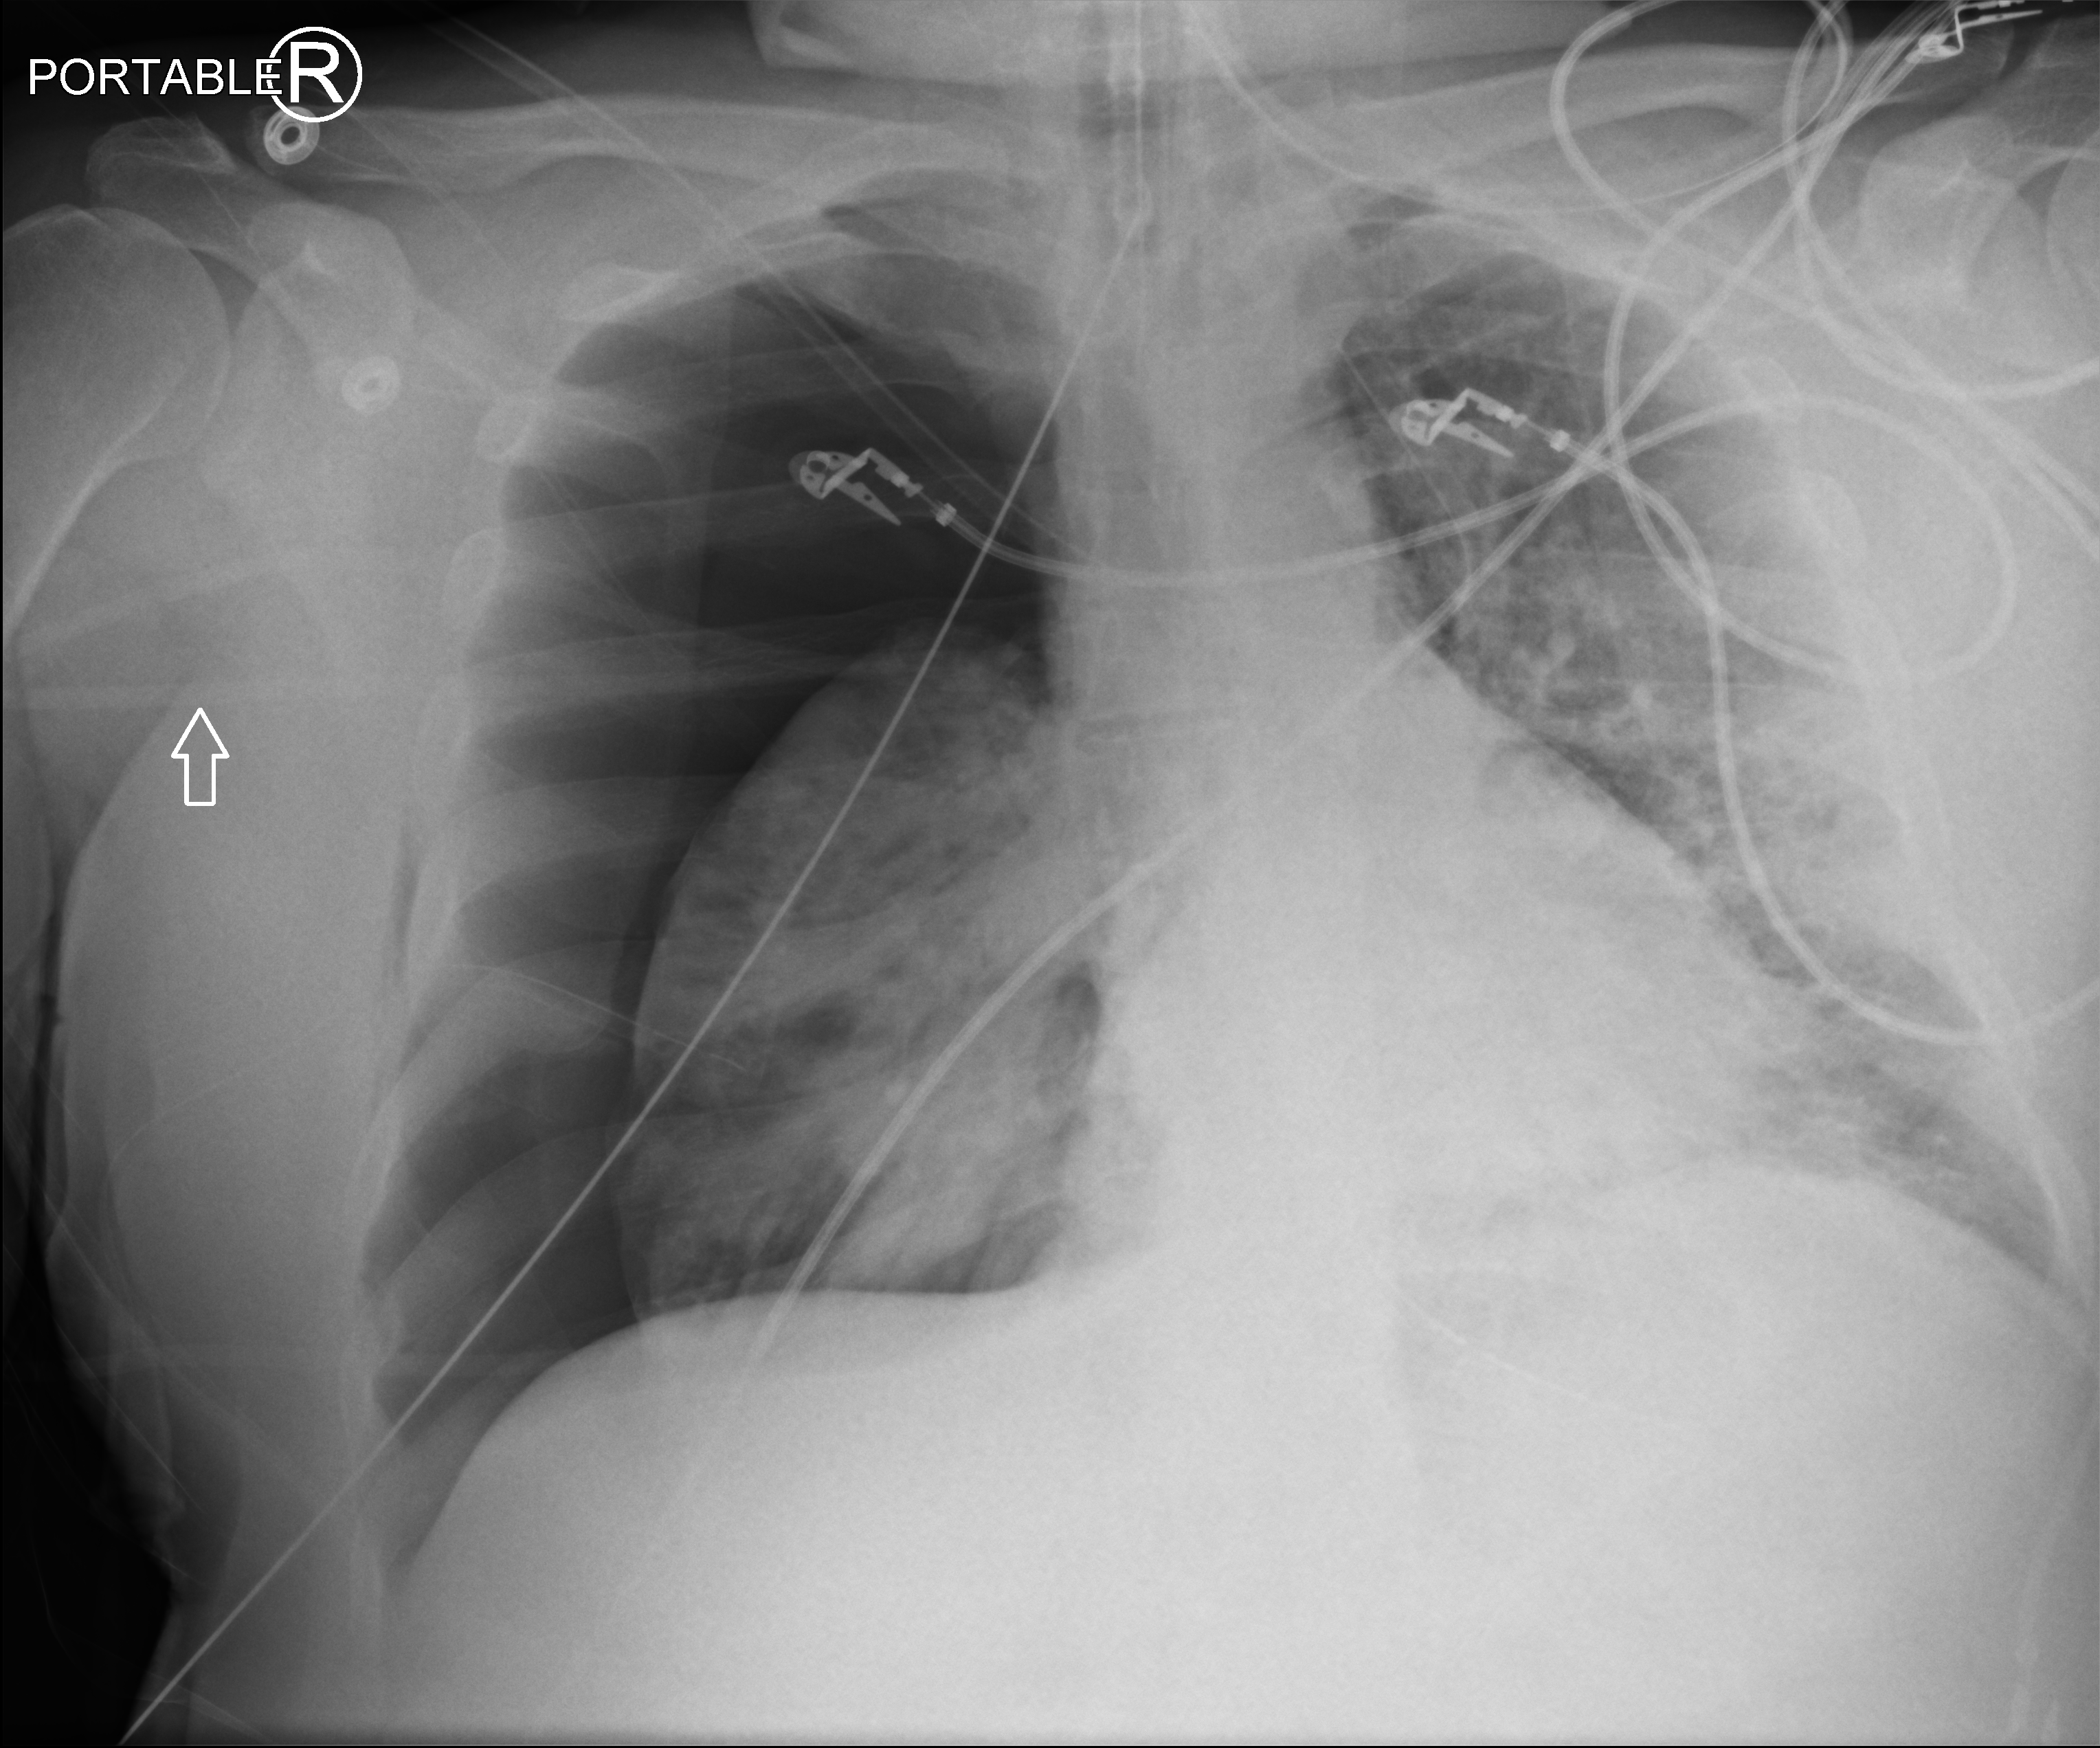
Portable chest radiograph; anteroposterior (AP) projection. Patient hospitalised with COVID-19; male, aged 18–59 years.
Admission-level facts for this patient (not findings on this image; timing relative to this image not recorded):
- admitted to intensive care during this hospital stay: yes
- chronic kidney disease (admission record): no